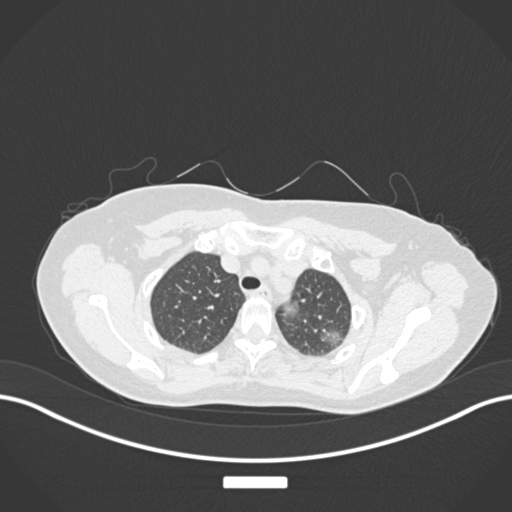
Chest CT, one axial slice. Reconstruction kernel B30f. 120 kVp. Lung window (W 1500 / L -600 HU). 512 × 512 image matrix, field of view 400 × 400 mm. Female patient, age 58 years. From the clinical record (not read from this slice): clinical TNM (as recorded): T1c N0 M0.
Annotated regions visible in this slice (rectangle marked by the reading radiologist):
- lung tumour (recorded histology: adenocarcinoma): box from (x=319, y=325) to (x=344, y=350) px